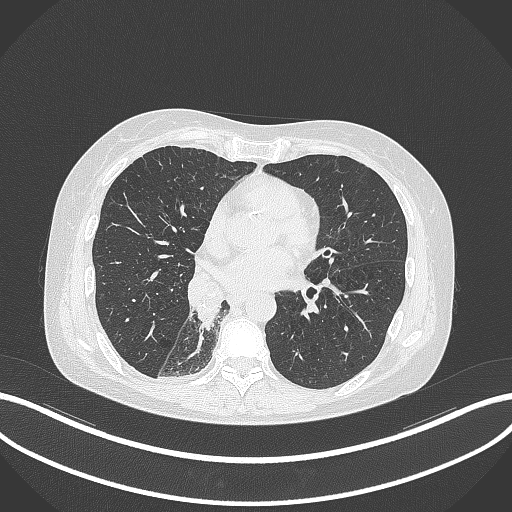
Chest CT, one axial slice; position 140 of 329 along the scan axis; reconstruction kernel B70f; 120 kVp; lung window (W 1500 / L -600 HU); 1 mm slice thickness; 512 × 512 image matrix, field of view 400 × 400 mm. Patient: female, 63 years. From the clinical record (not read from this slice): clinical TNM (as recorded): T1c N0 M0.
Annotated regions visible in this slice (rectangle marked by the reading radiologist):
- lung tumour (recorded histology: adenocarcinoma): box from (x=194, y=277) to (x=226, y=329) px